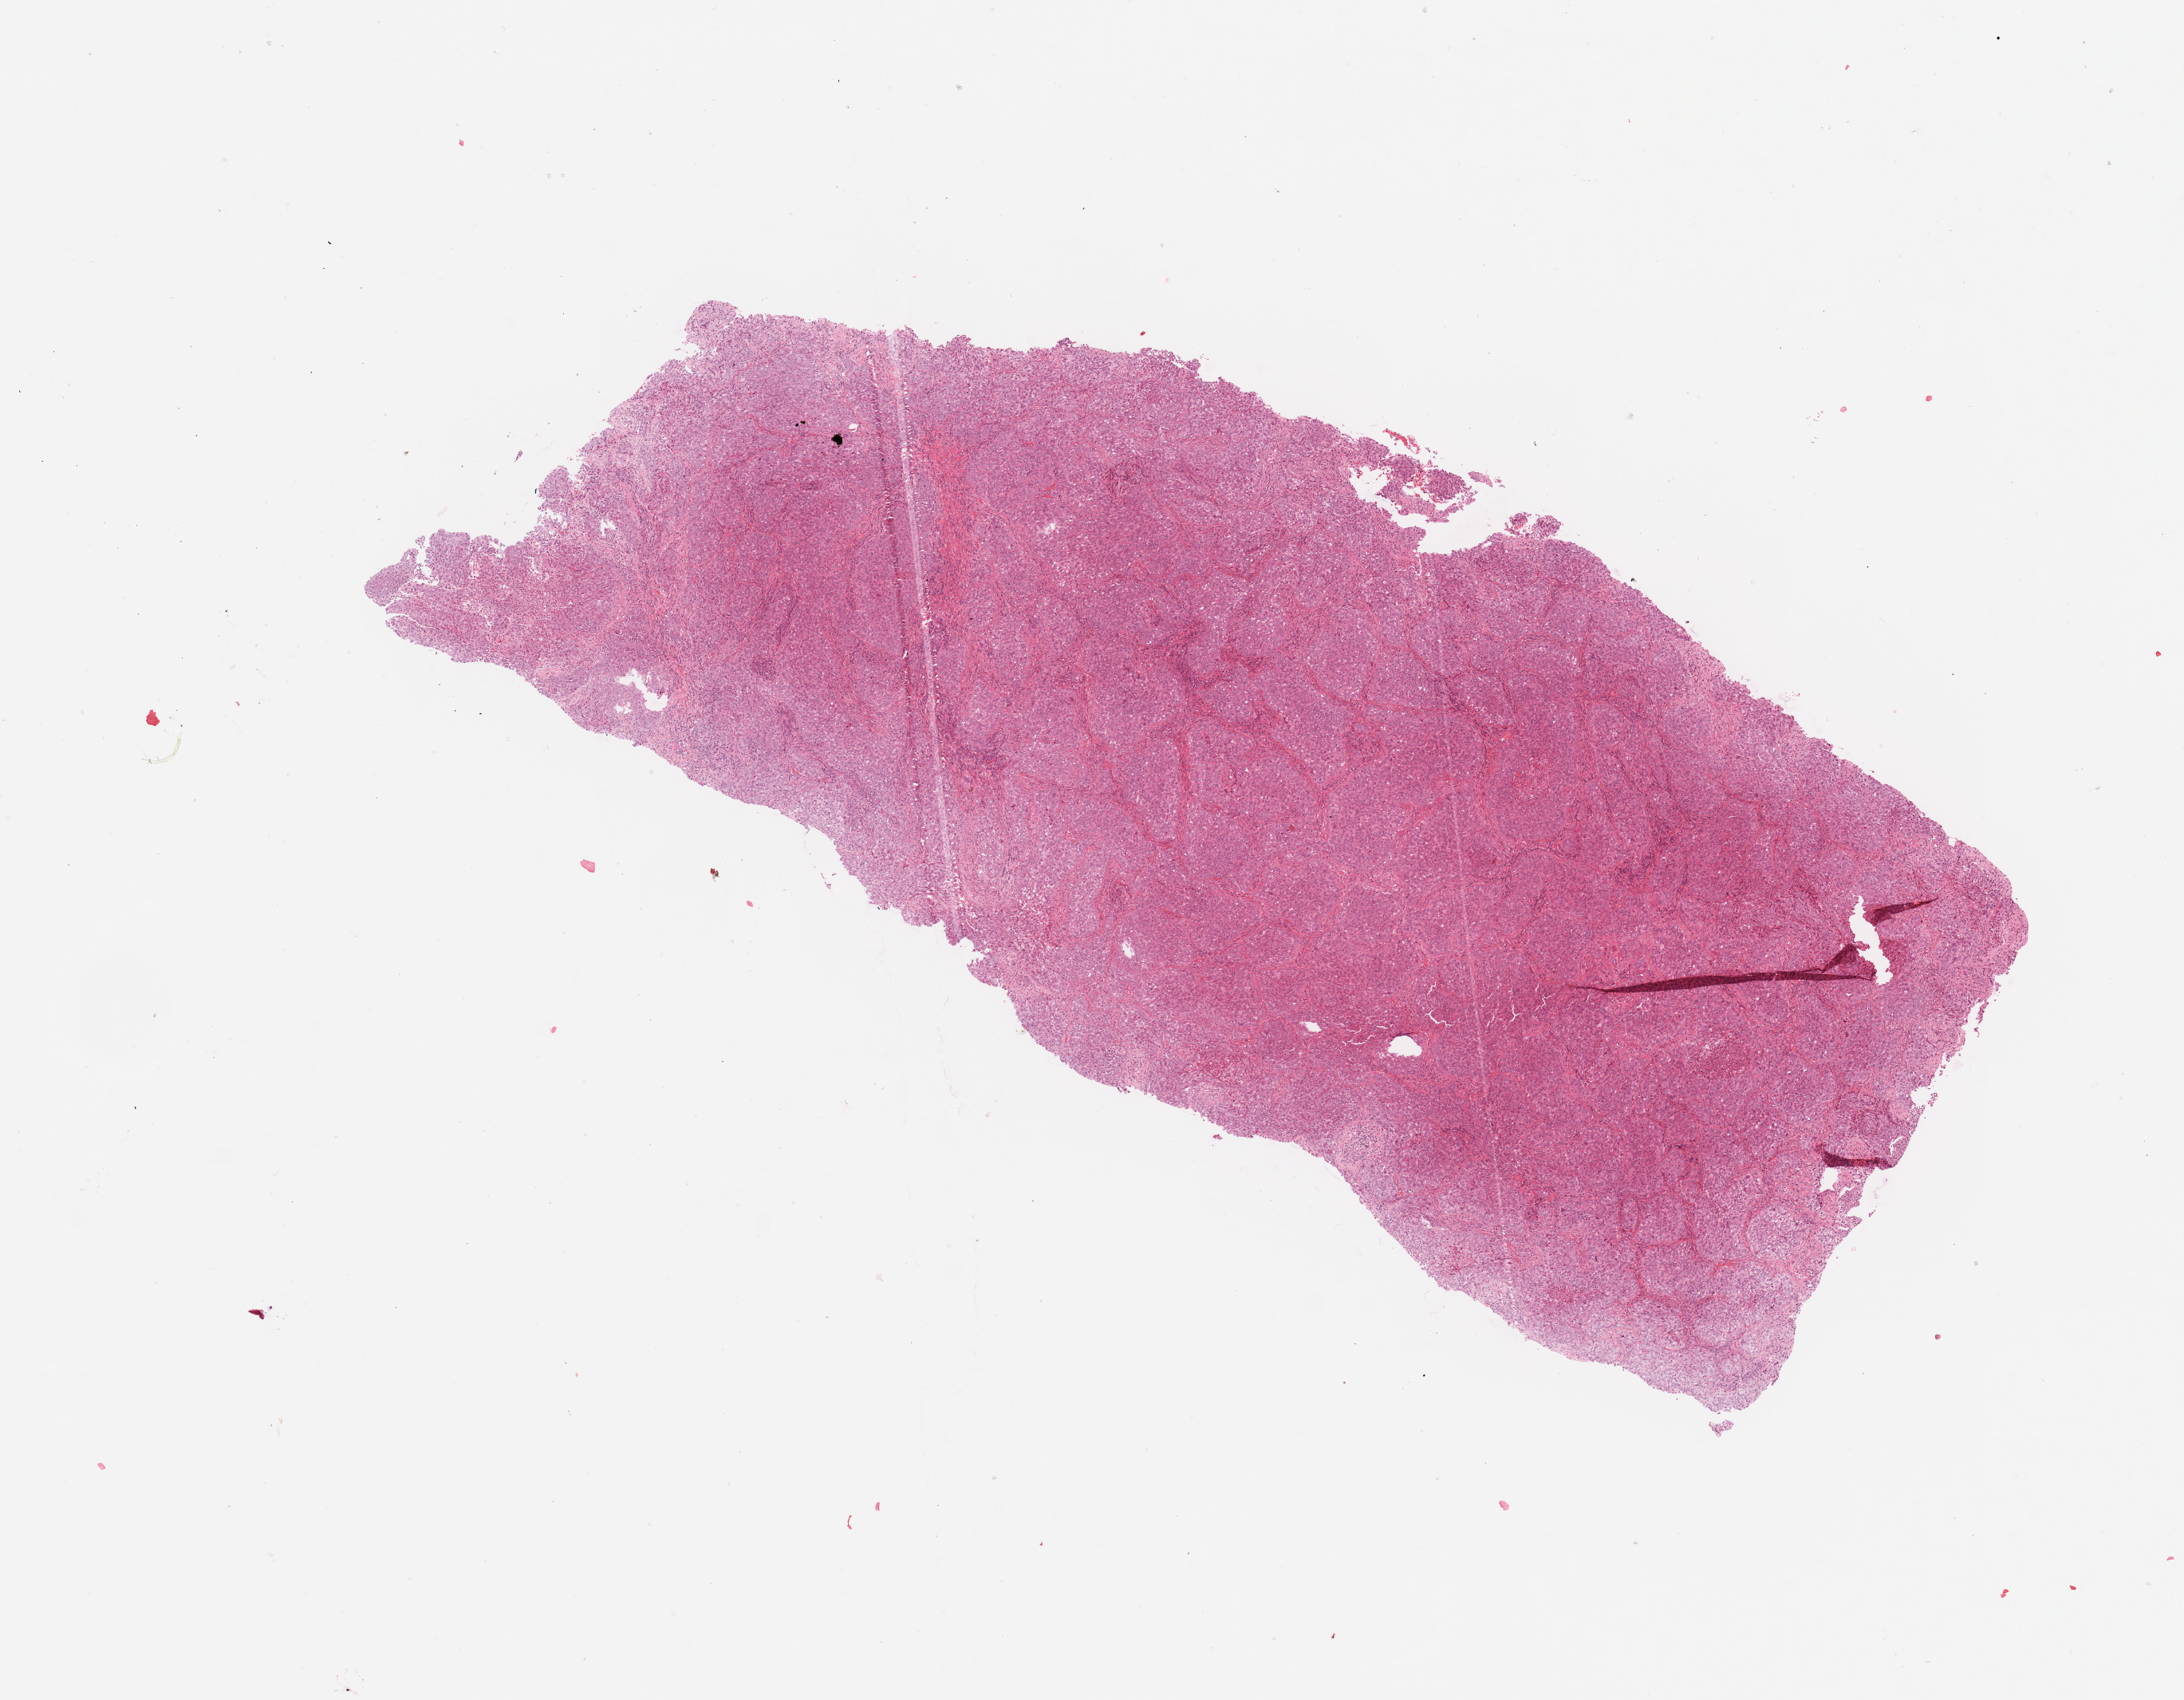
Whole-slide histology image, Hematoxylin and eosin (H&E) stained — whole scanned area (about 10.8 x 8.4 mm) shown as a low-resolution overview; tumour tissue sample, sampled site: lung. Female, 43 y/o. Histologic grade: G3 (poorly differentiated). Pathologist review of this section (percent, as recorded): tumour nuclei 85%, necrosis 0%.
AJCC pathologic stage: IIIA. Diagnosis: Adenocarcinoma, NOS.